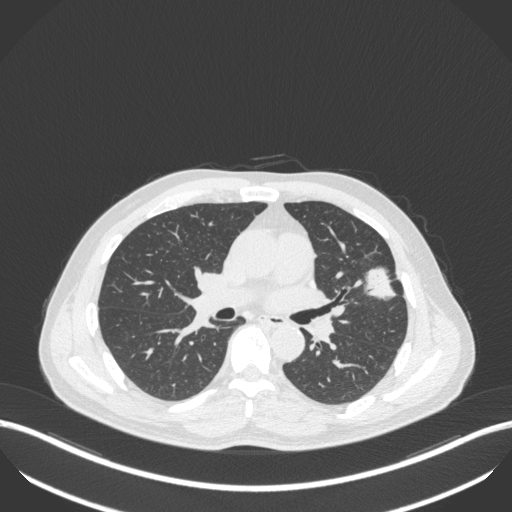
Chest CT, one axial slice; position 222 of 418 along the scan axis; reconstruction kernel B31f; 120 kVp; lung window (W 1500 / L -600 HU); 1 mm slice thickness; 512 × 512 image matrix, field of view 400 × 400 mm. Male patient, age 55 years. From the clinical record (not read from this slice): clinical TNM (as recorded): T1c N0 M0; histopathological grade: G2-3.
Outlined on this slice (bounding box drawn by a radiologist):
- lung tumour (recorded histology: adenocarcinoma): box from (x=364, y=262) to (x=404, y=307) px